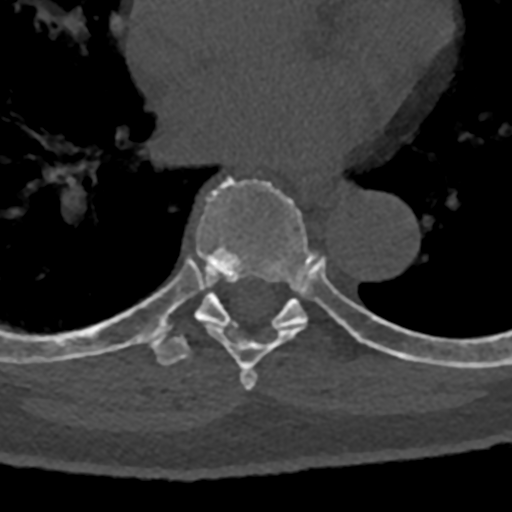
CT including the spine, one axial slice. Position 740 of 797 along the scan axis. Bone window (W 1800 / L 400 HU). 512 × 512 image matrix, field of view 160 × 160 mm. Patient: male, 74 years. Case-level facts recorded for this patient, not image findings: primary cancer: renal.
Annotated regions visible in this slice (semi-automatically segmented with operator editing):
- T6 vertebra: bounding box [x1, y1, x2, y2] px = [253, 376, 257, 380]
- T7 vertebra: [144, 176, 394, 390]
- T8 vertebra: [70, 278, 432, 366]